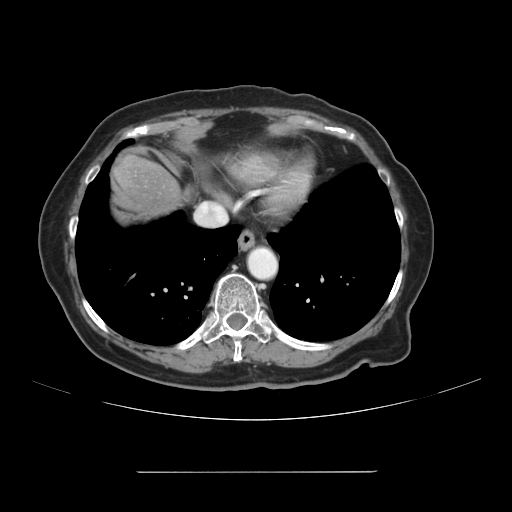
Contrast-enhanced abdominal CT, one axial slice; slice 103 of 111 in the series (ordered by position); 120 kVp; soft-tissue window (W 400 / L 40 HU); 2.5 mm slice thickness; 512 × 512 image matrix, field of view 400 × 400 mm. Female patient, age 74 years. Case-level facts recorded for this patient, not image findings: diagnosis: colorectal cancer liver metastases, imaged before liver resection; multiple liver metastases: yes; largest metastasis: 1.1 cm; disease in both lobes: yes.
Outlined on this slice (expert manual segmentation):
- liver: bounding box (x1, y1, x2, y2) in pixels: (109, 153, 182, 219)